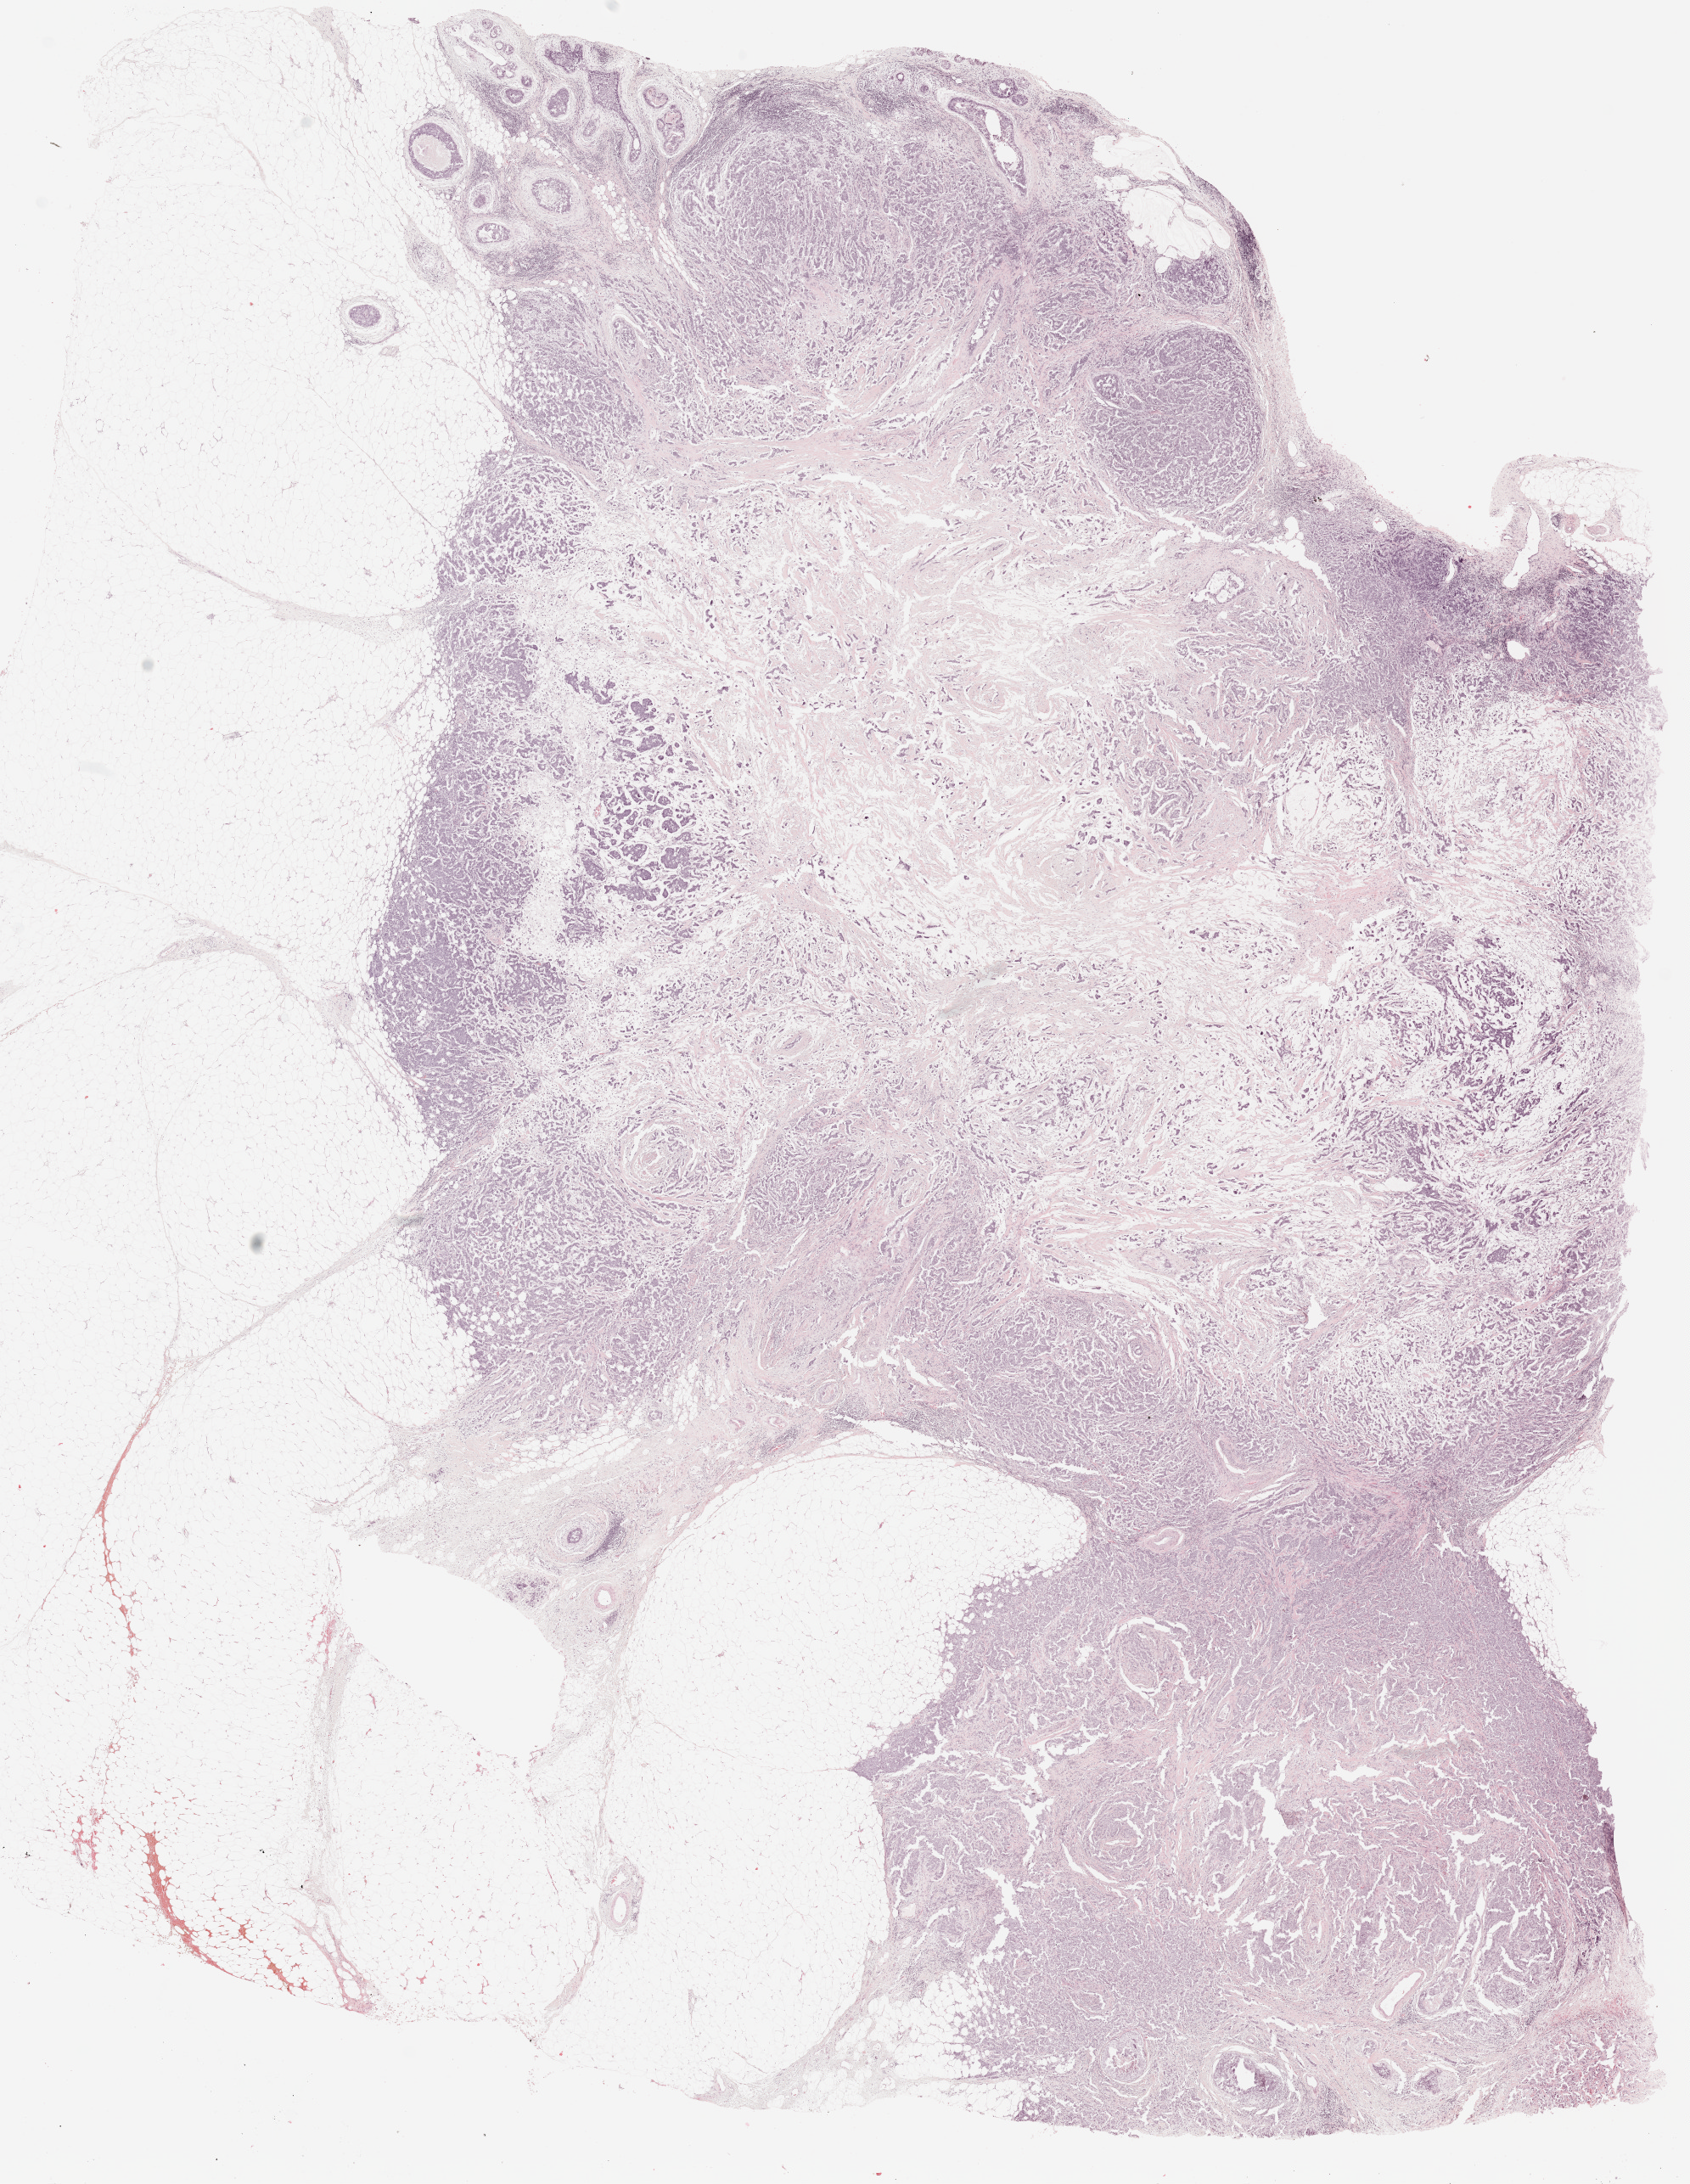
H&E whole-slide image — shown as a low-resolution overview of the whole scanned area (about 15.9 x 20.6 mm, from a 20x scan), formalin-fixed paraffin-embedded (FFPE) diagnostic section, breast, primary tumour sample. Female patient; age at initial diagnosis 38 years.
• lymph nodes positive (case pathology): 0 of 18 examined
• AJCC pathologic stage: IIA (5th edition)
• histologic diagnosis: Infiltrating duct mixed with other types of carcinoma